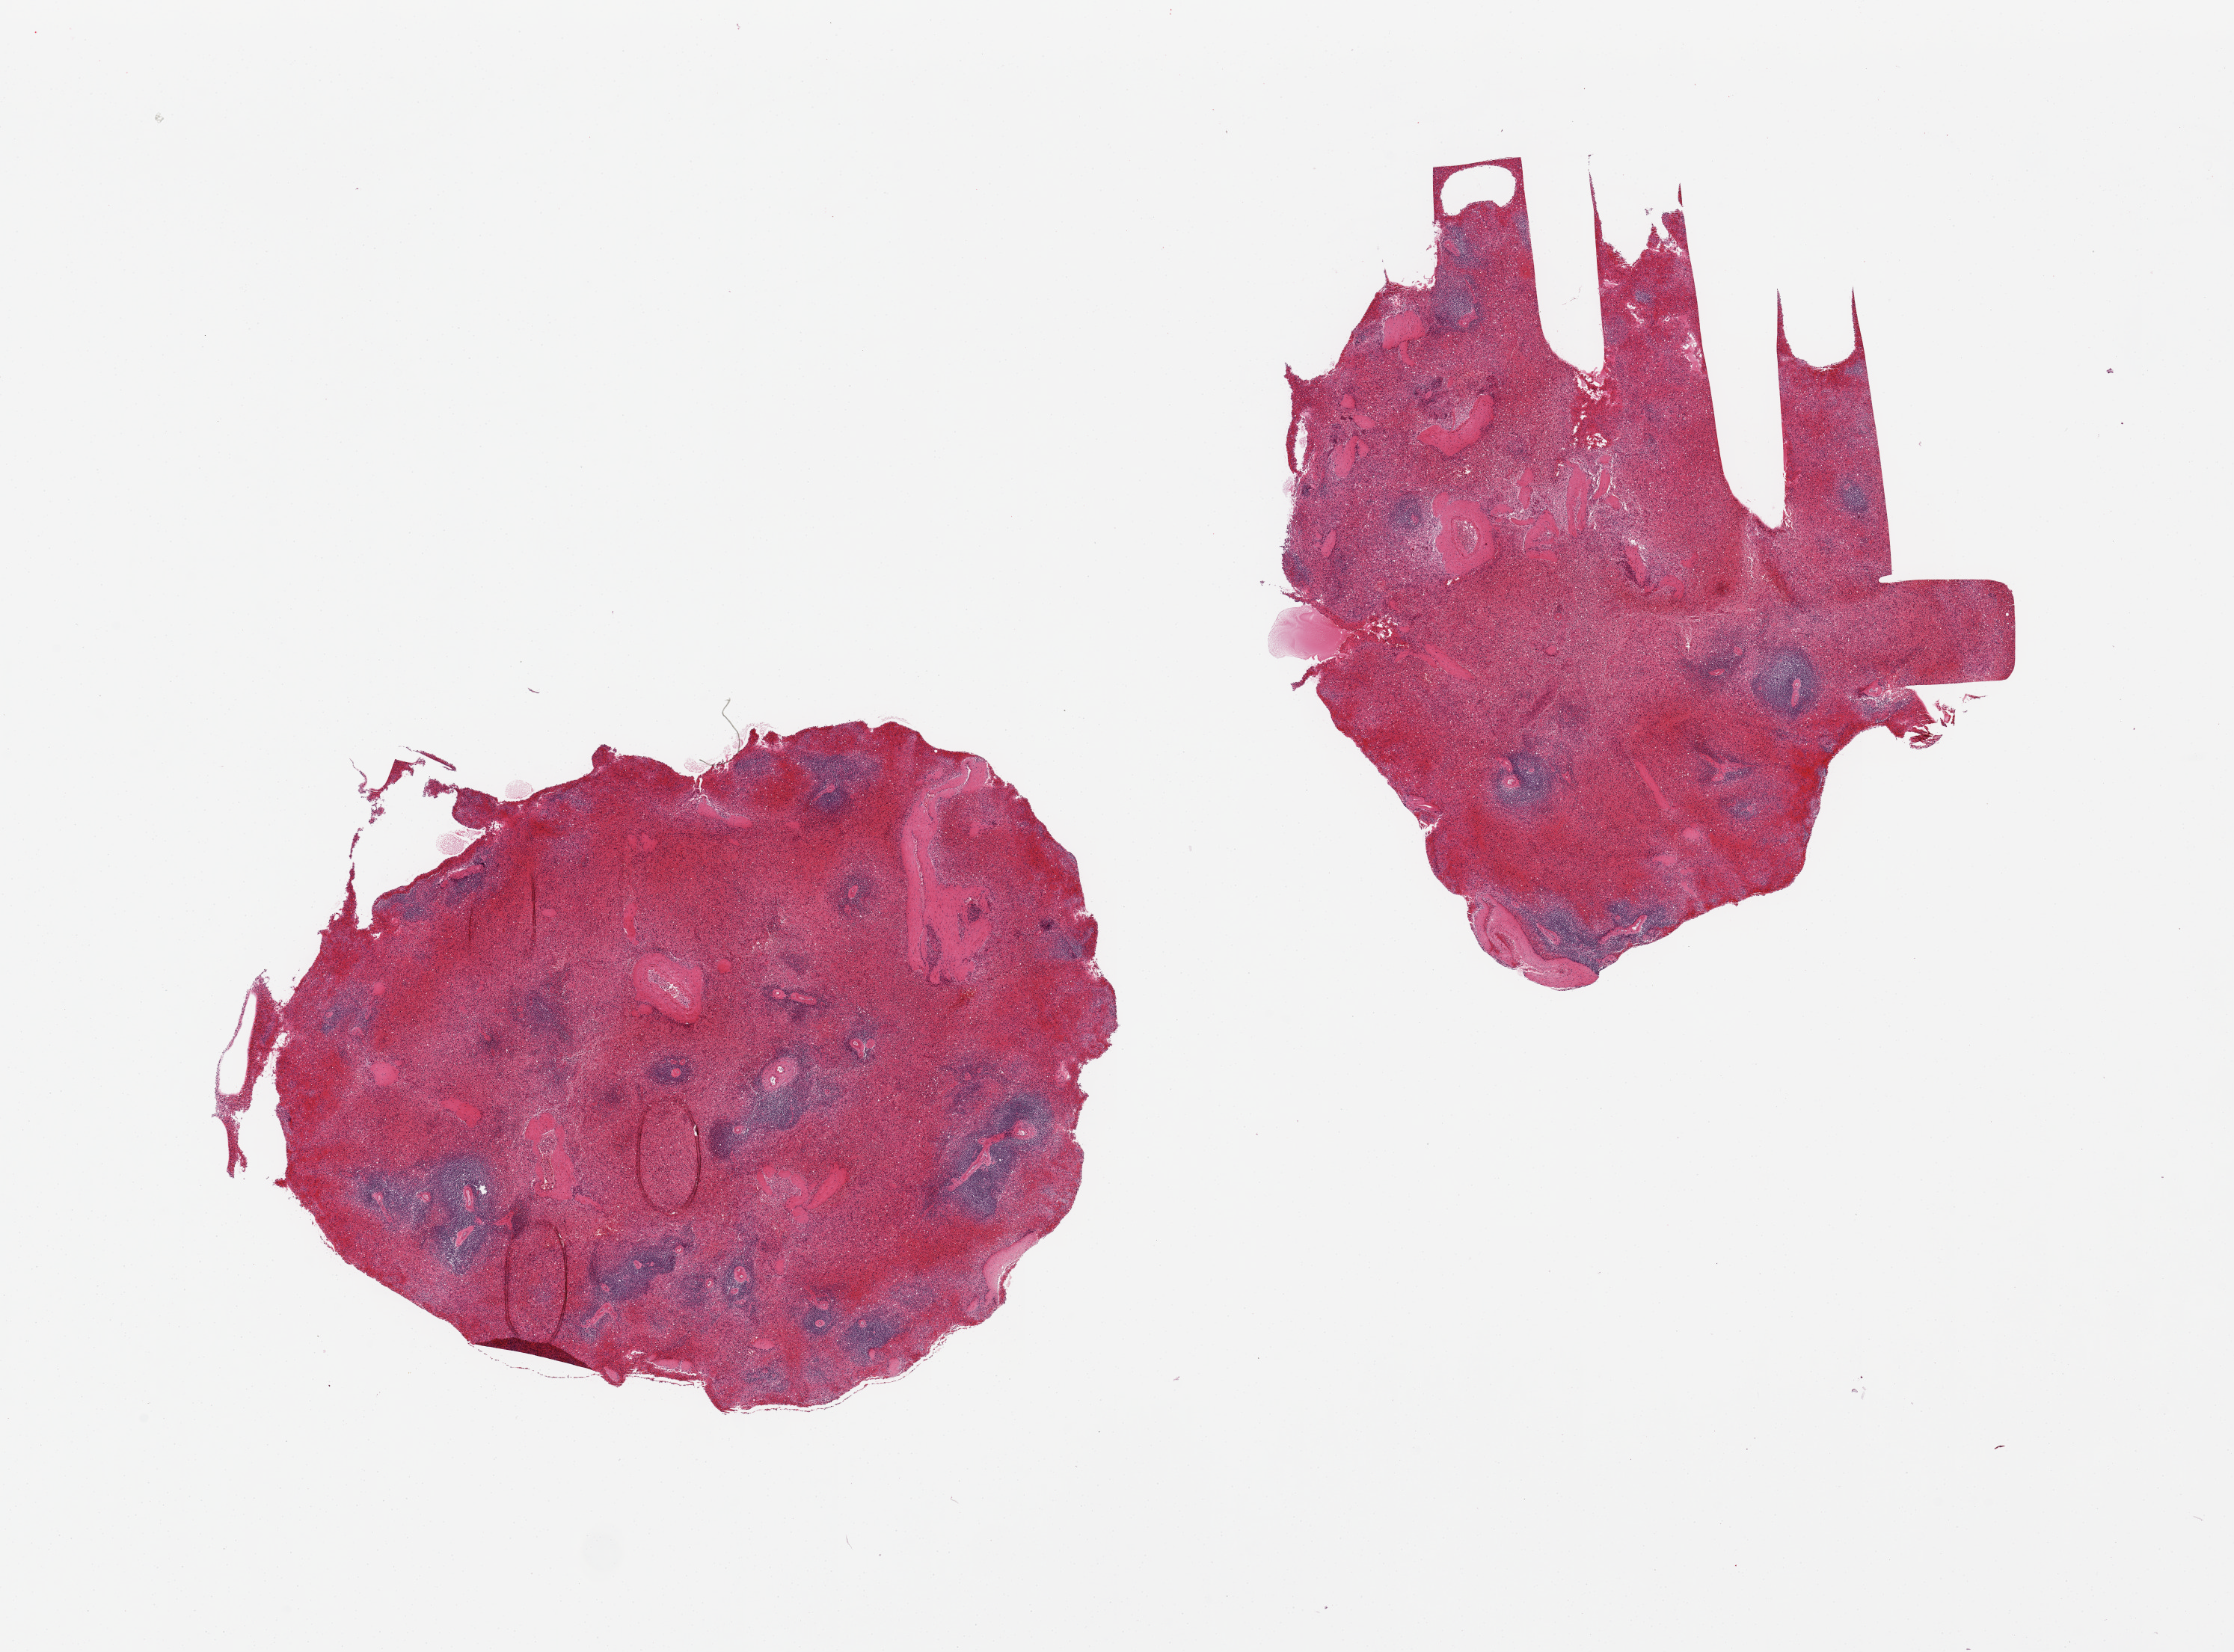
Whole-slide image, H&E stain, a low-resolution overview of the entire scanned area, about 23.6 x 17.5 mm; PAXgene-fixed, paraffin-embedded tissue; sampled site (target tissue): spleen; donor tissue sample. Donor: female.
Pathologist's review note for this sample: 2 pieces, moderate congestion.